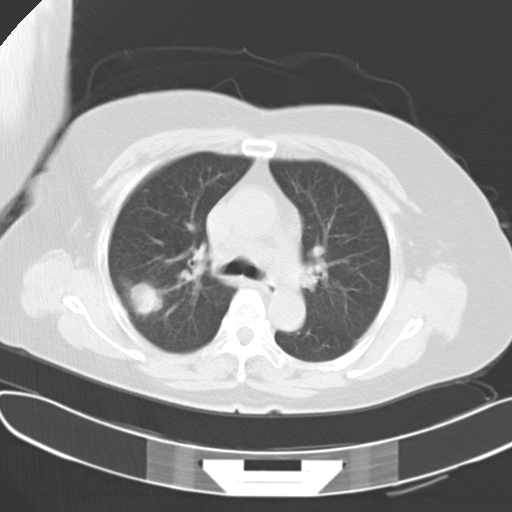
Chest CT, one axial slice. Reconstruction kernel B40f. 120 kVp. Lung window (W 1500 / L -600 HU). 512 × 512 image matrix, field of view 367 × 367 mm. Patient: female, 63 years. From the clinical record (not read from this slice): clinical TNM (as recorded): T1c N3 M1a.
Outlined on this slice (rectangle marked by the reading radiologist):
- lung tumour (recorded histology: adenocarcinoma): bounding box [x1, y1, x2, y2] px = [125, 277, 166, 322]